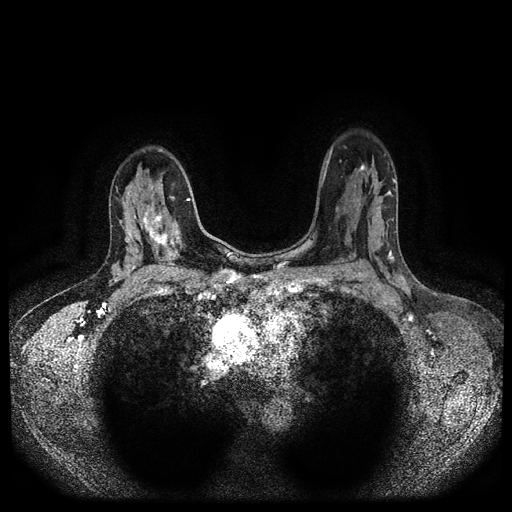
Breast MRI (dynamic contrast-enhanced, multi-phase), one axial slice. Slice 68 of 116 in the series (ordered by position). Dynamic contrast-enhanced series, time point 2 of 5 at this slice position (early post-contrast). 1.5 T. TE 2.6 ms, TR 5.4 ms. 2 mm slice thickness. 512 × 512 image matrix. Patient: female, 47 years.
Annotated regions visible in this slice (semi-automatic segmentation, software-assisted and operator-edited):
- breast lesion (labelled 'tumour' in the annotation; benign lesions carry a separate 'benign' label): bounding box <139,199,183,251> (left, top, right, bottom; pixels)